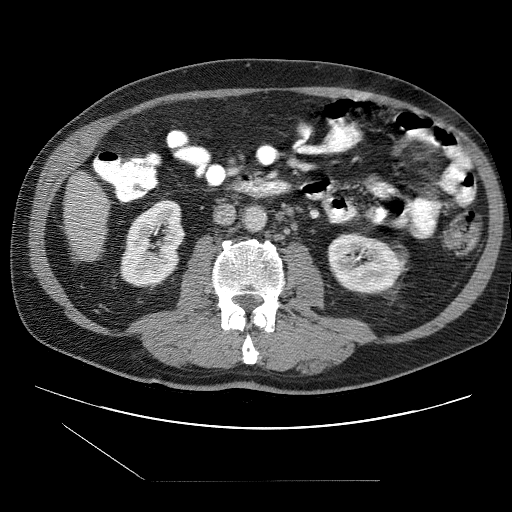
Contrast-enhanced abdominal CT (liver protocol), one axial slice. Position 14 of 109 along the scan axis. Reconstruction kernel STANDARD. One of 2 acquisitions stored at this slice position. Soft-tissue window (W 400 / L 40 HU). 512 × 512 image matrix, field of view 400 × 400 mm. From the clinical record (not read from this slice): diagnosis: hepatocellular carcinoma (patient treated with transarterial chemoembolisation; whether this scan precedes or follows treatment is not stated here); TNM stage (as recorded): Stage-IIIB; Child-Pugh class: A; tumour differentiation: well differentiated.
Outlined on this slice (semi-automatic segmentation, software-assisted and operator-edited):
- liver parenchyma outside the tumour (the mass and vessels are separate outlines, so this box may not span the whole liver): bounding box <64,172,108,262> (left, top, right, bottom; pixels)